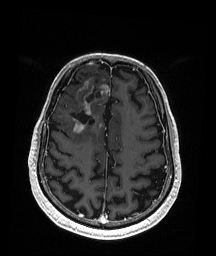
Brain MRI from a brain-tumour surgery series, one axial slice; position 61 of 192 along the scan axis; T1-weighted post-contrast; 1 mm slice thickness; 216 × 256 image matrix, field of view 211 × 250 mm. Case-level facts recorded for this patient, not image findings: histopathology: Astrocytoma; WHO grade: 3; IDH mutation: yes; tumour location: Right Frontal.
Structures marked on this image (manually delineated by an expert):
- previous resection cavity: box from (x=70, y=81) to (x=101, y=124) px
- tumour: (x=71, y=81)–(x=110, y=137)